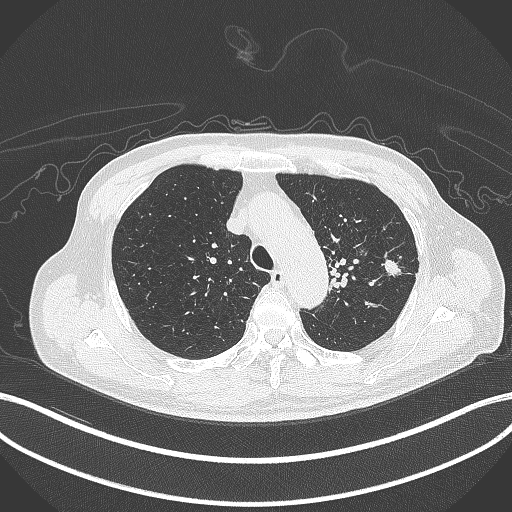
Chest CT, one axial slice. Position 333 of 417 along the scan axis. 120 kVp. Lung window (W 1500 / L -600 HU). 512 × 512 image matrix, field of view 400 × 400 mm. Patient: male, 77 years. Case-level facts recorded for this patient, not image findings: clinical TNM (as recorded): T3 N1 M0.
Structures marked on this image (rectangle marked by the reading radiologist):
- lung tumour (recorded histology: adenocarcinoma): bounding box (x1, y1, x2, y2) in pixels: (380, 257, 405, 278)